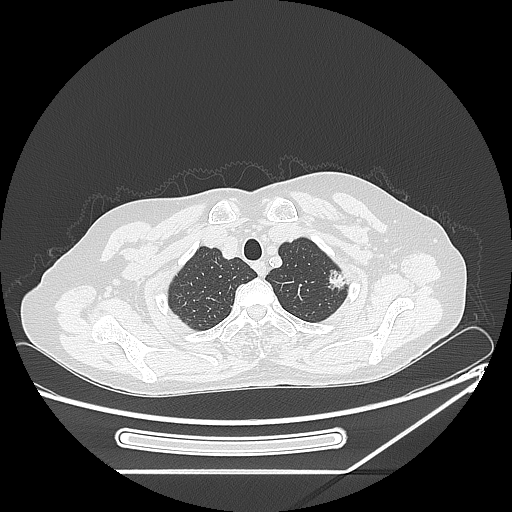
Chest CT, one axial slice; reconstruction kernel LUNG; 120 kVp; lung window (W 1500 / L -600 HU); 1.25 mm slice thickness; 512 × 512 image matrix. Female patient, age 57 years. From the clinical record (not read from this slice): clinical TNM (as recorded): T1c N0 M0; histopathological grade: G2-3.
Outlined on this slice (rectangle marked by the reading radiologist):
- lung tumour (recorded histology: adenocarcinoma): bounding box (x1, y1, x2, y2) in pixels: (324, 267, 345, 292)